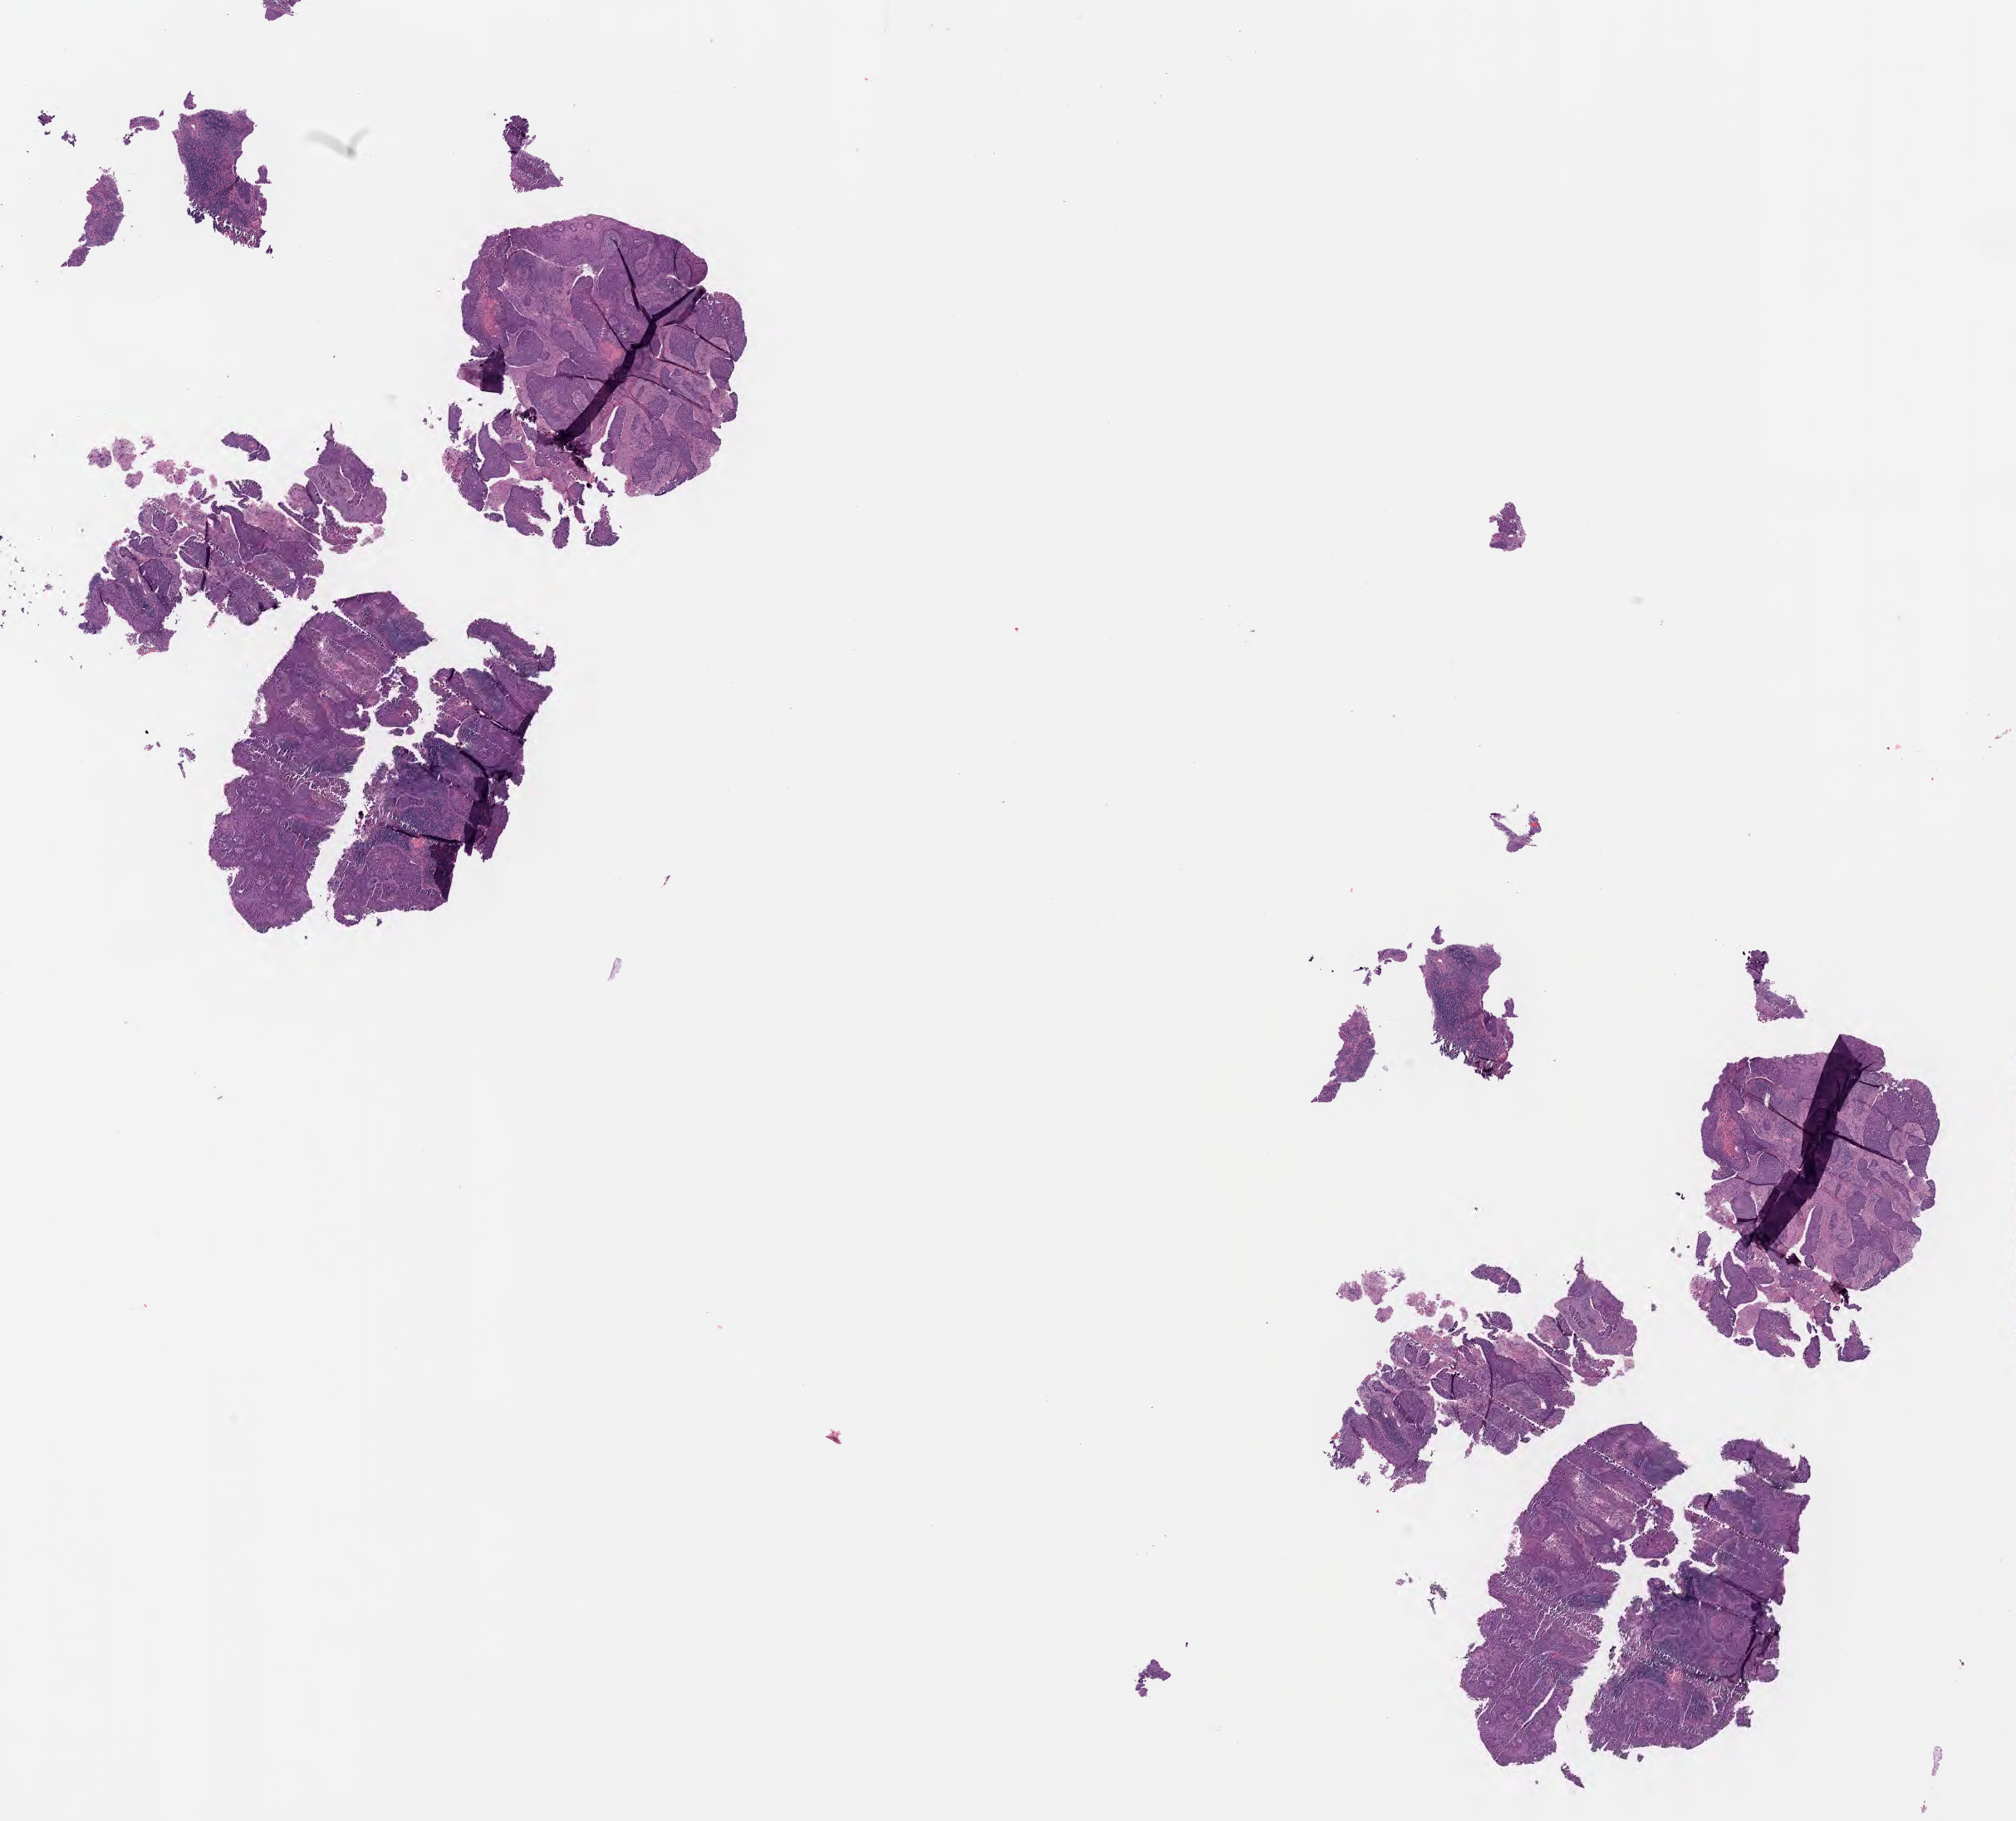
H&E whole-slide image, shown as a low-resolution overview of the whole scanned area (about 19.6 x 17.7 mm), tumor tissue, site: cervix. Patient female; age 49 years.
• diagnosis: Squamous cell carcinoma, large cell, nonkeratinizing, NOS